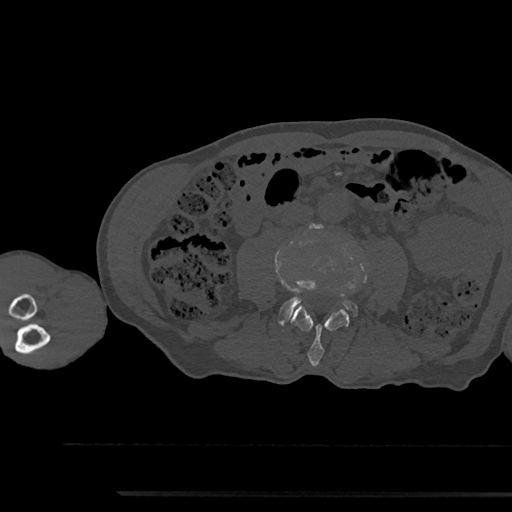
CT including the spine, one axial slice; position 452 of 797 along the scan axis; 120 kVp; bone window (W 1800 / L 400 HU); 0.5 mm slice thickness; 512 × 512 image matrix, field of view 367 × 367 mm. Patient: male, 79 years. Case-level facts recorded for this patient, not image findings: primary cancer: prostate.
Outlined on this slice (semi-automatic segmentation, software-assisted and operator-edited):
- L3 vertebra: box from (x=292, y=306) to (x=349, y=366) px
- L4 vertebra: (x=279, y=280)–(x=357, y=324)